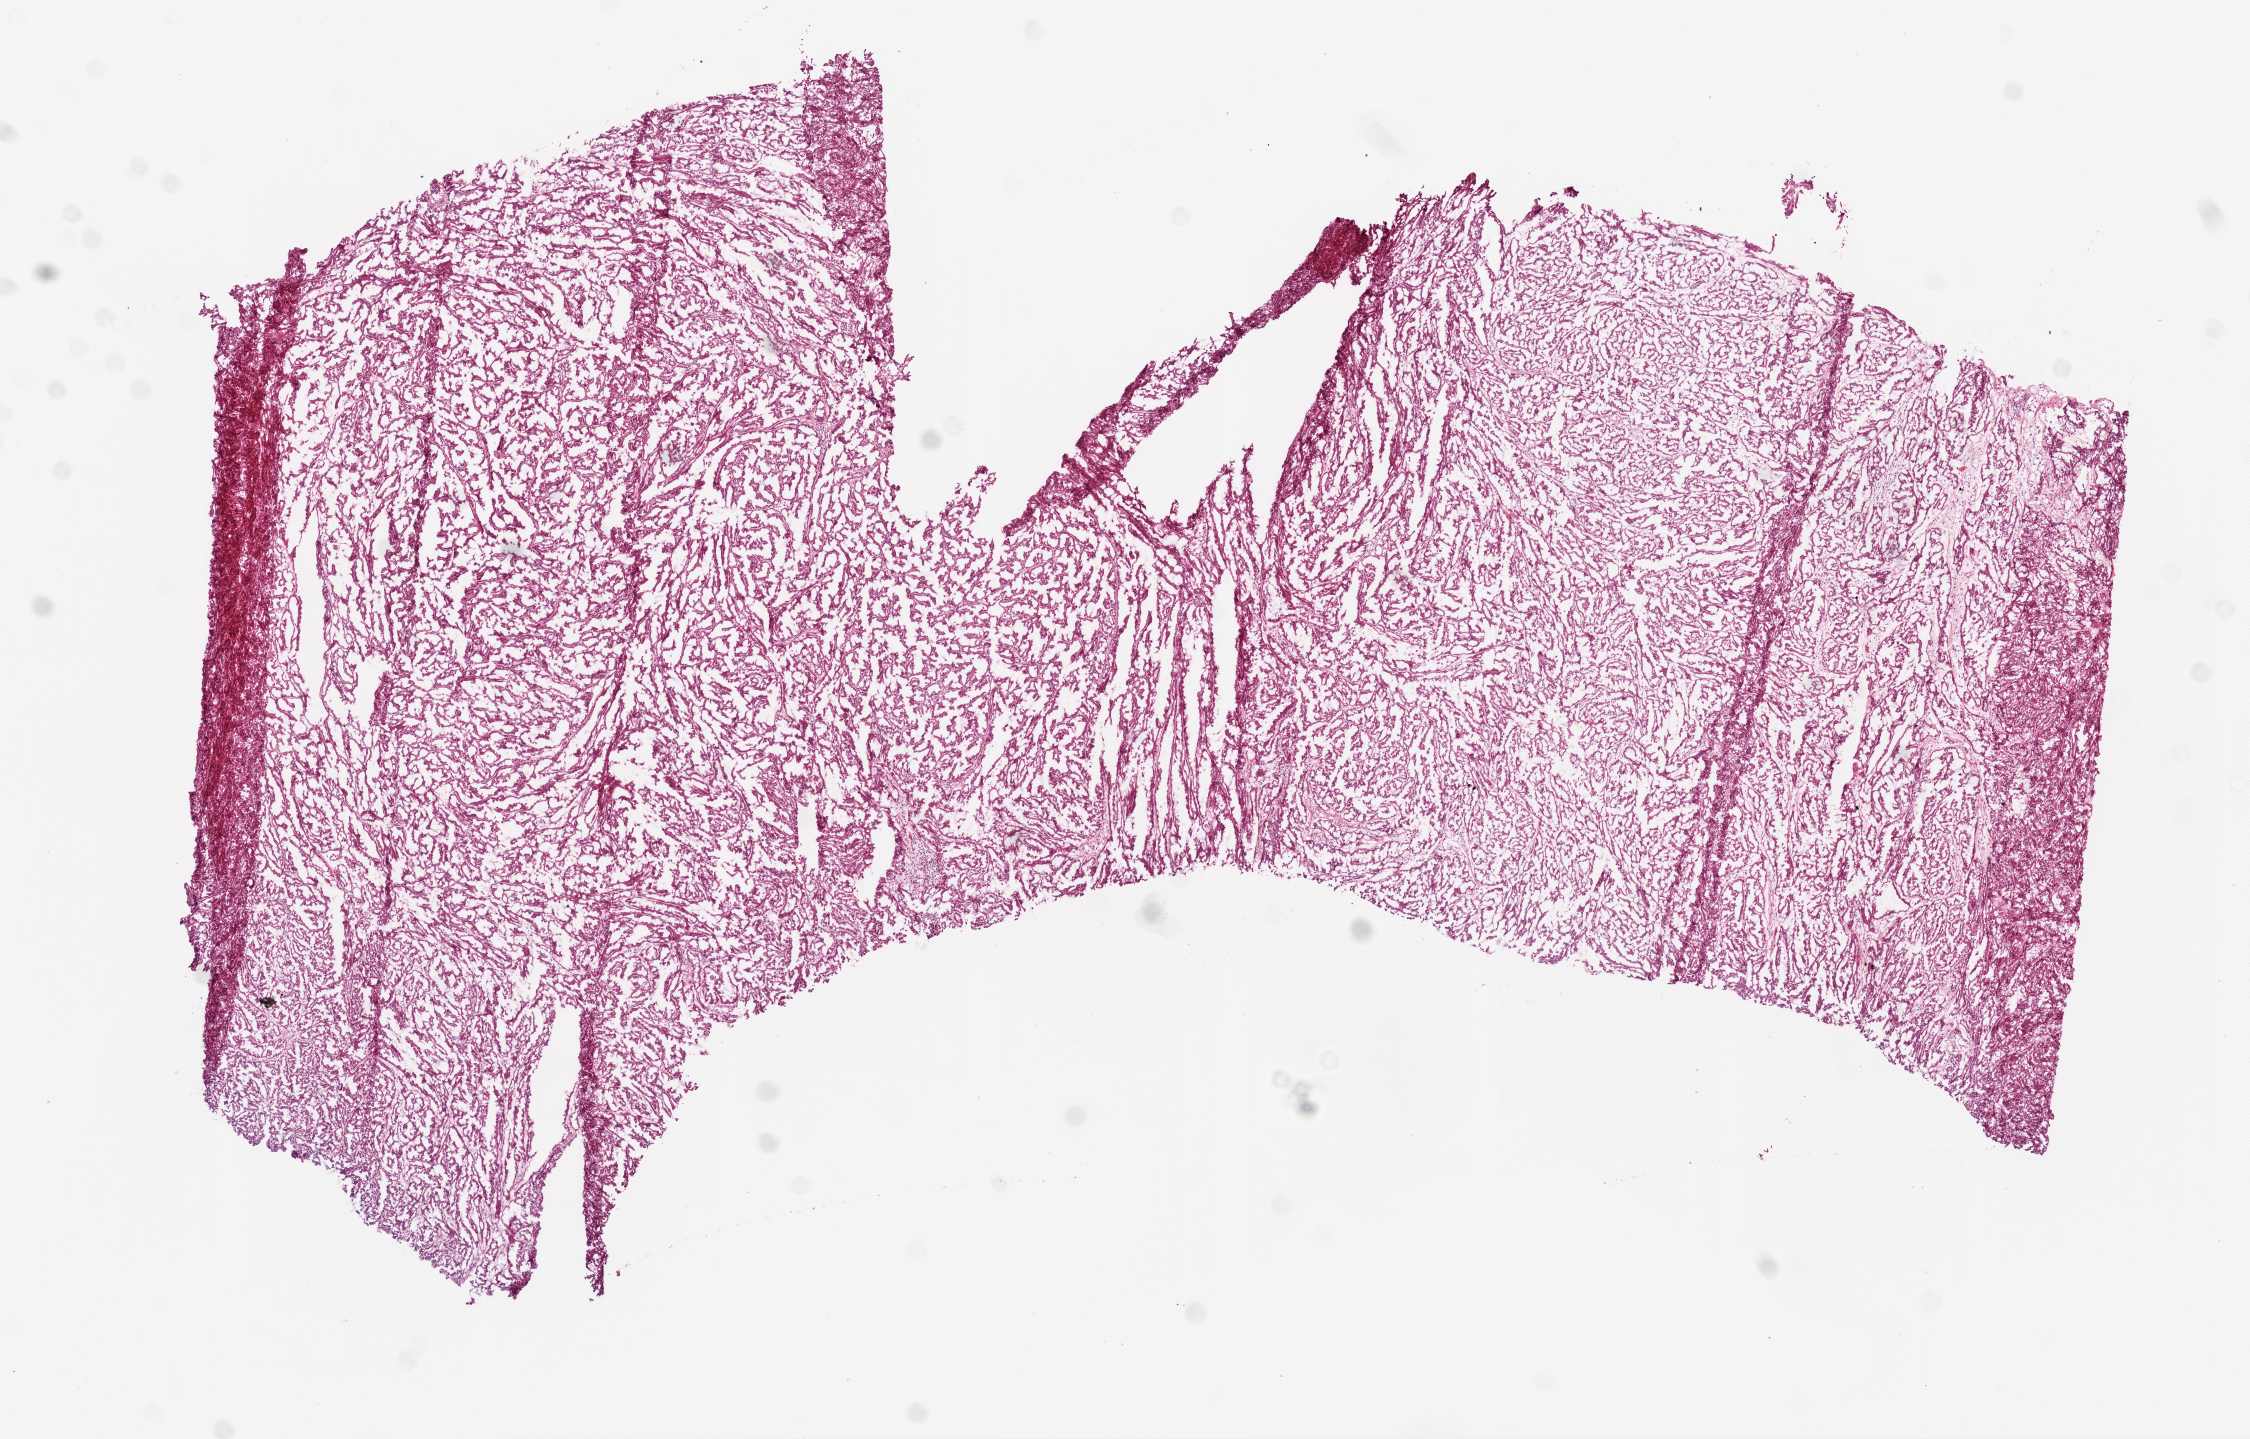
Digitized H&E-stained tissue section (whole slide) — a low-resolution overview of the entire scanned area, about 9.0 x 5.8 mm (slide scanned at 20x), frozen section, sample: primary tumour, kidney. Male patient; age at initial diagnosis 41 years. Pathologist review of this section (percent, as recorded): tumour cells 85%, tumour nuclei 75%, normal cells 0%, stromal cells 15%, necrosis 0%.
Histologic diagnosis: Papillary adenocarcinoma, NOS.